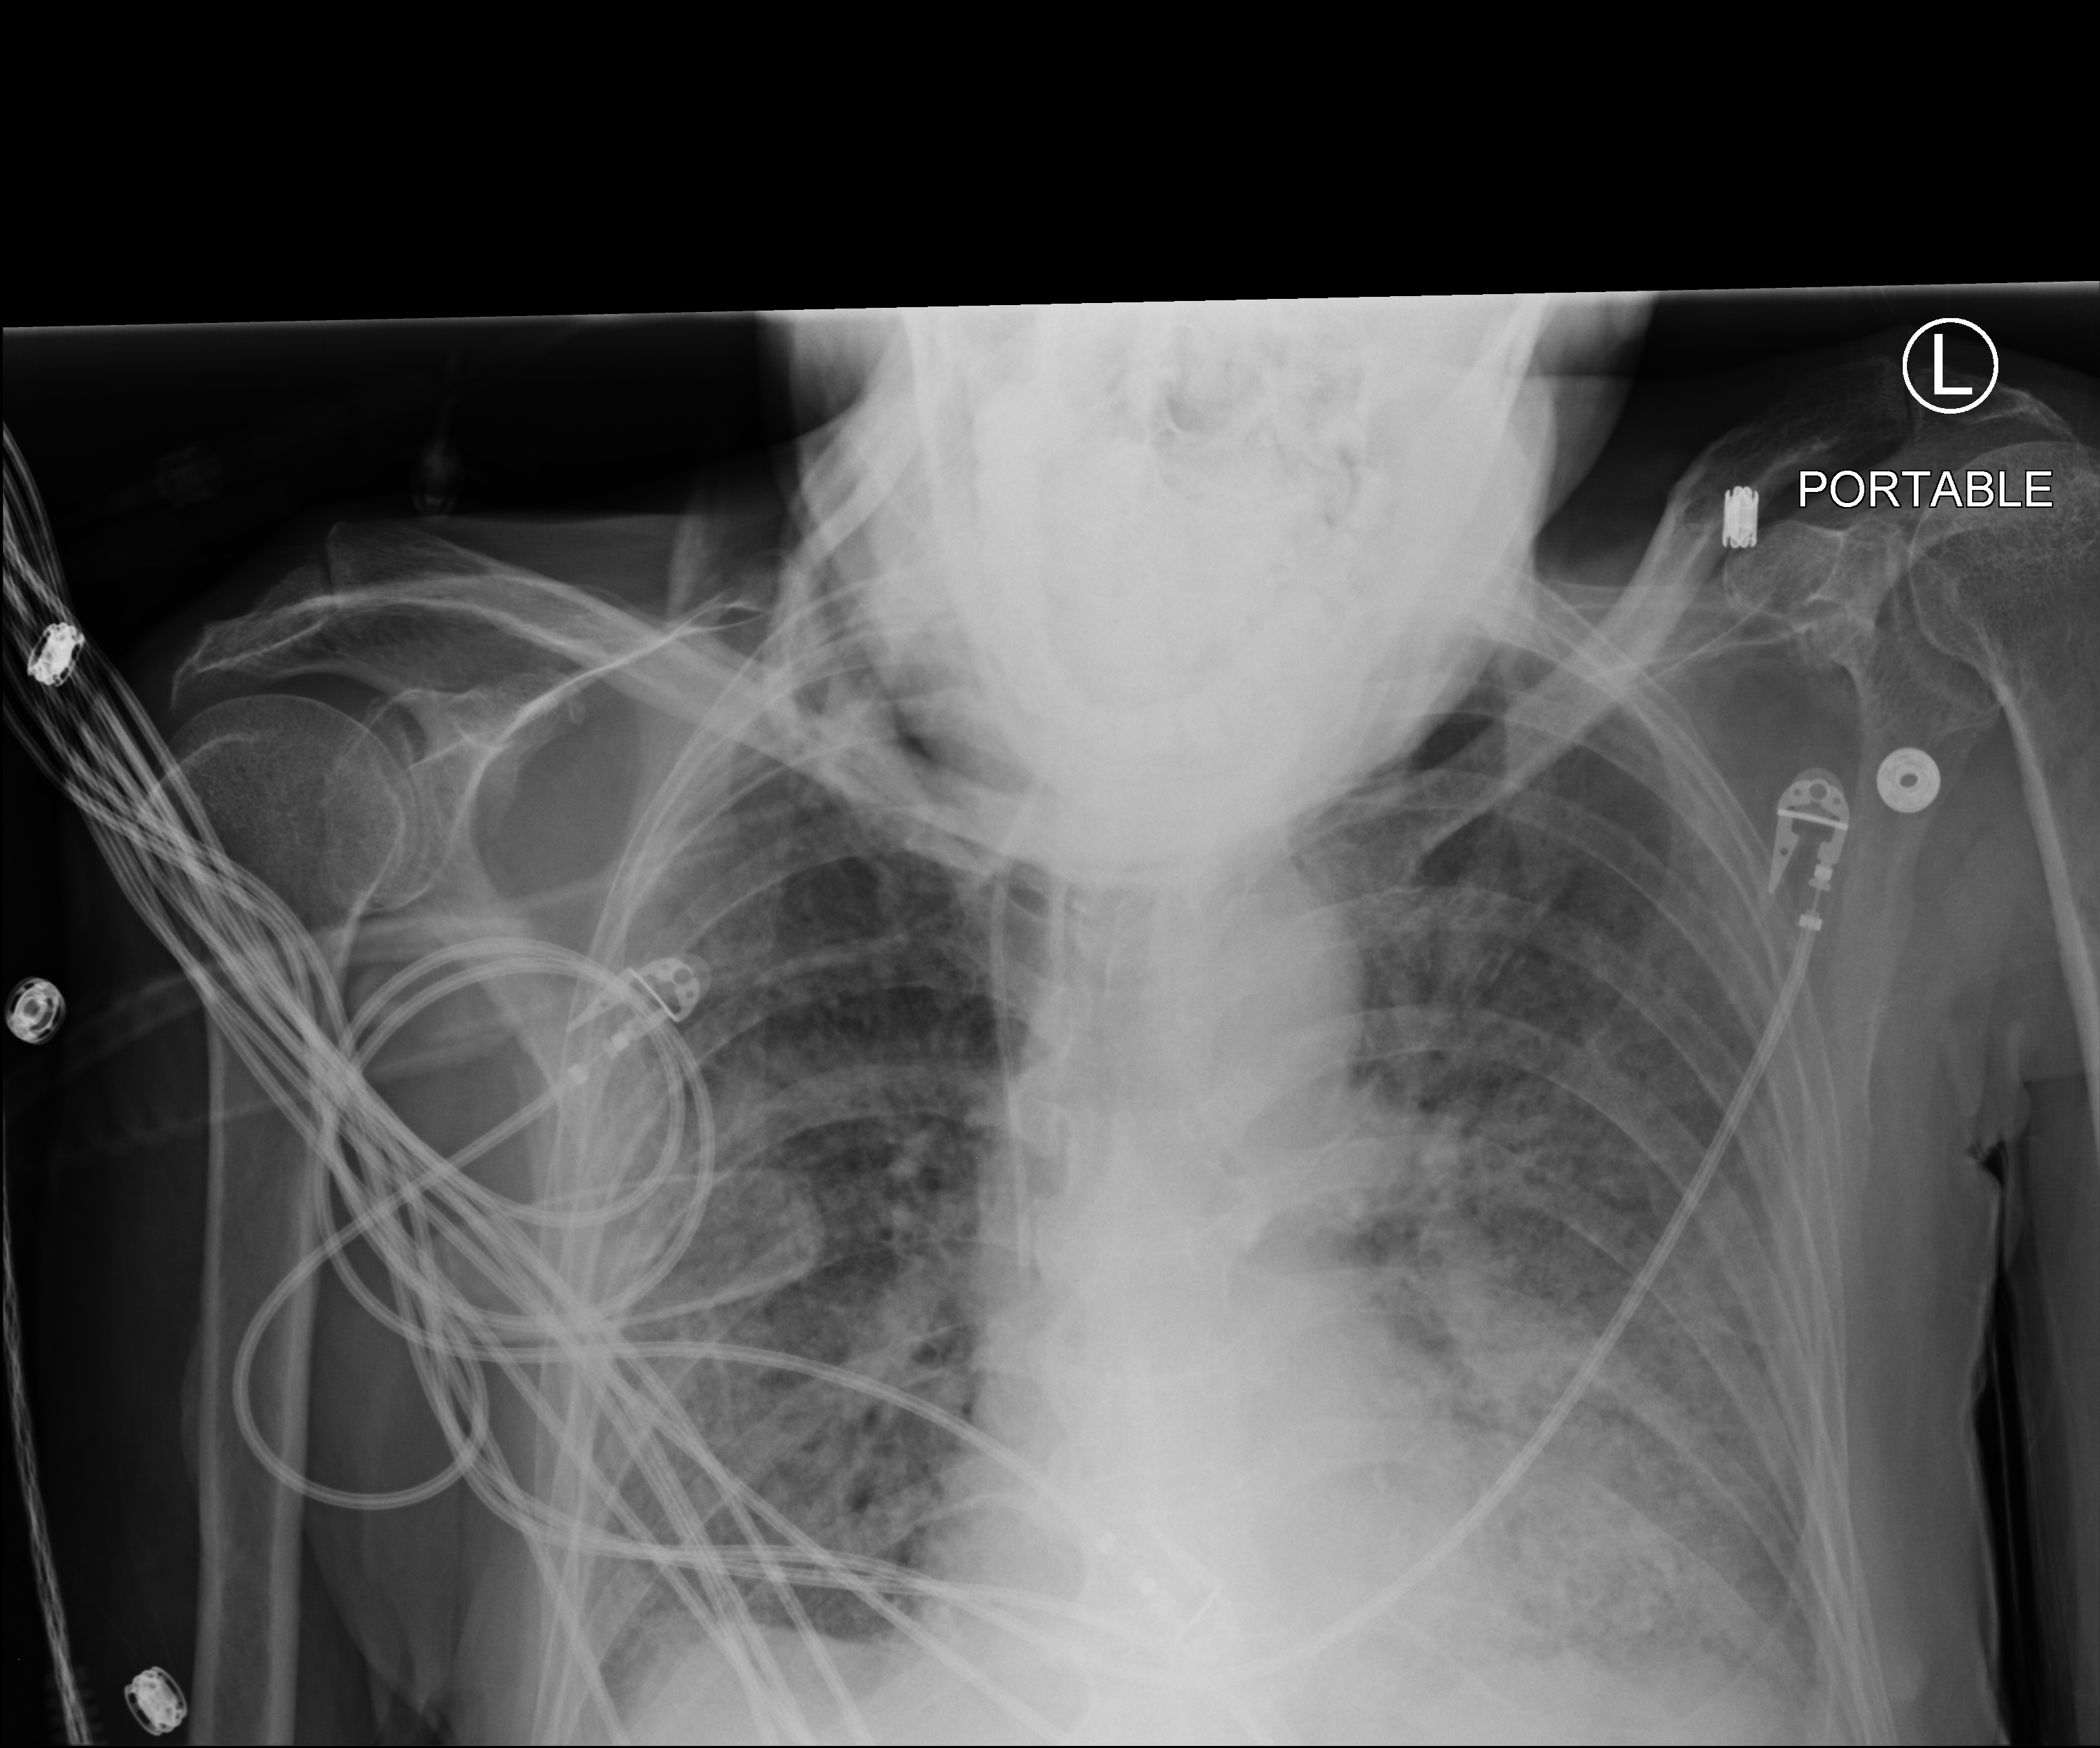
Portable chest radiograph; anteroposterior (AP) projection. Patient hospitalised with COVID-19; male, aged 60–74 years.
From the hospital-stay record, not from the radiograph (when in the stay this image was taken is not recorded): hypertension (admission record): yes.